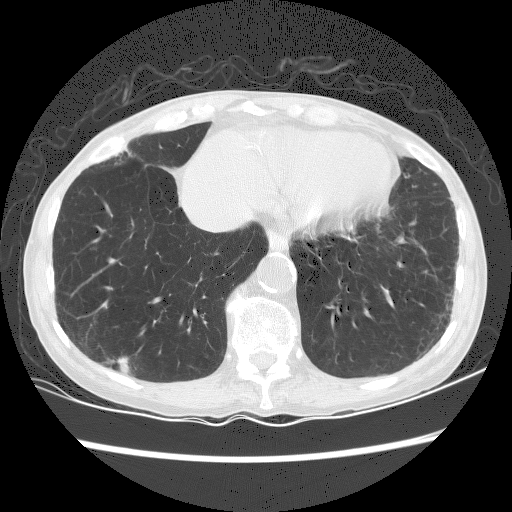
Low-dose screening chest CT, one axial slice. 120 kVp. Lung window (W 1500 / L -600 HU). 512 × 512 image matrix, field of view 320 × 320 mm.
Structures marked on this image (manually delineated by an expert):
- lesion 1 (tumor, lower lobe of right lung): bounding box (x1, y1, x2, y2) in pixels: (105, 357, 130, 373)